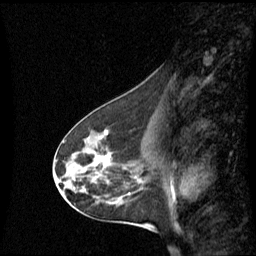
Breast MRI (dynamic contrast-enhanced), one sagittal slice; slice 31 of 60 in the series (ordered by position); dynamic contrast-enhanced series, image 2 of 3 at this slice position (ordered by acquisition); 1.5 T; TE 4.2 ms, TR 8.4 ms; 2.2 mm slice thickness; 256 × 256 image matrix, field of view 240 × 240 mm. Patient: female, 45 years. Case-level facts recorded for this patient, not image findings: setting: breast cancer imaged before/during neoadjuvant chemotherapy; receptor status: HR-positive, HER2-negative.
Structures marked on this image (semi-automatic segmentation, software-assisted and operator-edited):
- analysis volume of interest (the breast-tissue region the enhancement analysis was run in; not a lesion): bounding box <60,126,149,215> (left, top, right, bottom; pixels)
- tumour enhancement mask (voxels above the 70 % enhancement threshold inside the analysis volume of interest): <93,130,140,181>